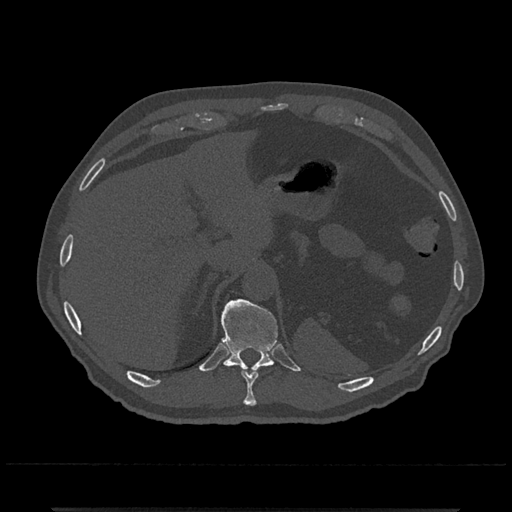
CT including the spine, one axial slice; position 515 of 797 along the scan axis; reconstruction kernel Br40s/3; 120 kVp; bone window (W 1800 / L 400 HU); 0.5 mm slice thickness; 512 × 512 image matrix, field of view 393 × 393 mm. Patient: male, 67 years. From the clinical record (not read from this slice): primary cancer: prostate.
Structures marked on this image (semi-automatic segmentation, software-assisted and operator-edited):
- T10 vertebra: bounding box [x1, y1, x2, y2] px = [241, 370, 259, 407]
- T11 vertebra: [218, 299, 278, 372]